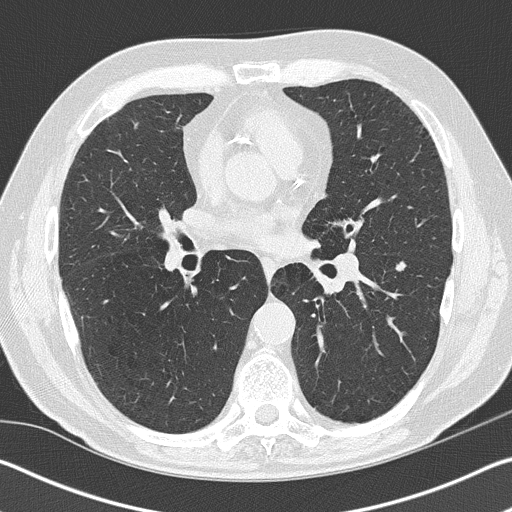
Axial slice from a low-dose chest CT screening exam; baseline annual screen; lung window (W 1500 / L -600 HU); 2 mm slice thickness; slice 82 of 161 in the series. Male, age 65 years at enrolment.
Expert reader's lesion annotation, box from (x=380, y=251) to (x=421, y=285) px. No non-calcified nodule or mass ≥4 mm was recorded by the screening reader at this exam. Official screen result: negative screen, minor abnormalities not suspicious for lung cancer. Later outcome: lung cancer diagnosed 460 days after this screen — non-small cell carcinoma, left lower lobe, right hilum, poorly differentiated (G3), stage IV (AJCC 6th edition), 5 mm at pathology.